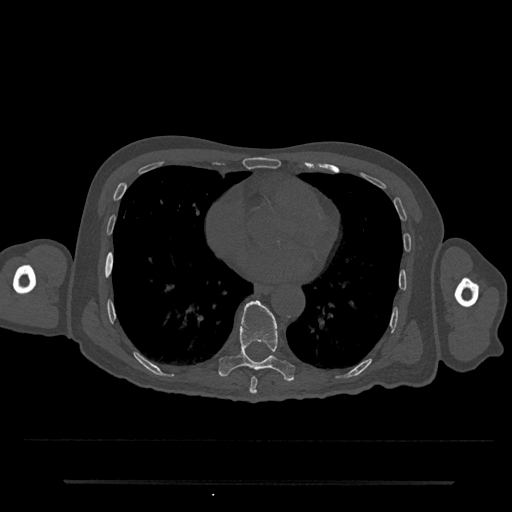
CT including the spine, one axial slice. Slice 373 of 797 in the series (ordered by position). 120 kVp. Bone window (W 1800 / L 400 HU). 0.5 mm slice thickness. 512 × 512 image matrix, field of view 427 × 427 mm. Male patient, age 74 years. Case-level facts recorded for this patient, not image findings: primary cancer: prostate.
Outlined on this slice (semi-automatic segmentation, software-assisted and operator-edited):
- T8 vertebra: bounding box <249,377,258,394> (left, top, right, bottom; pixels)
- T9 vertebra: <218,300,295,380>